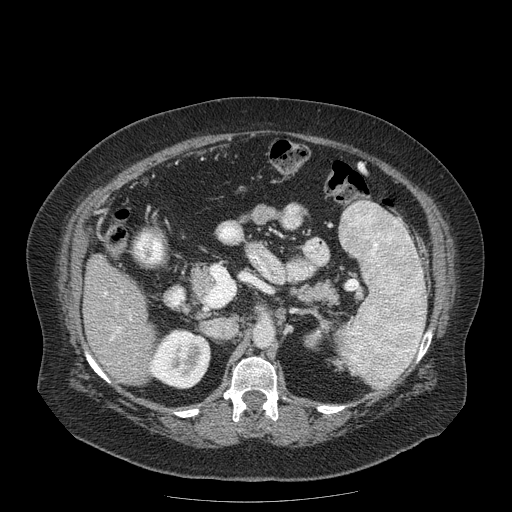
Contrast-enhanced abdominal CT (liver protocol), one axial slice; position 77 of 204 along the scan axis; 120 kVp; soft-tissue window (W 400 / L 40 HU); 2.5 mm slice thickness; 512 × 512 image matrix, field of view 440 × 440 mm. Case-level facts recorded for this patient, not image findings: diagnosis: hepatocellular carcinoma (patient treated with transarterial chemoembolisation; whether this scan precedes or follows treatment is not stated here); TNM stage (as recorded): Stage-IIIB; Child-Pugh class: A; tumour differentiation: well differentiated; tumour nodularity: uninodular.
Structures marked on this image (semi-automatic segmentation, software-assisted and operator-edited):
- liver parenchyma outside the tumour (the mass and vessels are separate outlines, so this box may not span the whole liver): bounding box <82,254,156,384> (left, top, right, bottom; pixels)
- liver vessels: <104,292,132,341>